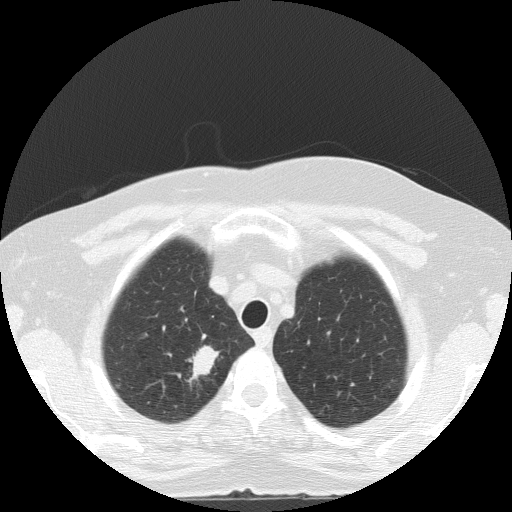
Axial slice from a low-dose chest CT screening exam, baseline annual screen, lung window (W 1500 / L -600 HU), 2 mm slice thickness, 120 kVp, 512 × 512 image matrix. Female participant, aged 56 years at enrolment. Current smoker at enrolment.
Expert-annotated lung lesion, bounding box [x1, y1, x2, y2] px = [172, 340, 232, 388]. The screening reader recorded 2 non-calcified nodules or masses ≥4 mm on this exam; which of them this box marks is not recorded. Participant outcome: lung cancer diagnosed 24 days after this screen — adenocarcinoma, NOS, right upper lobe, poorly differentiated (G3), stage IA (AJCC 6th edition), 20 mm at pathology.